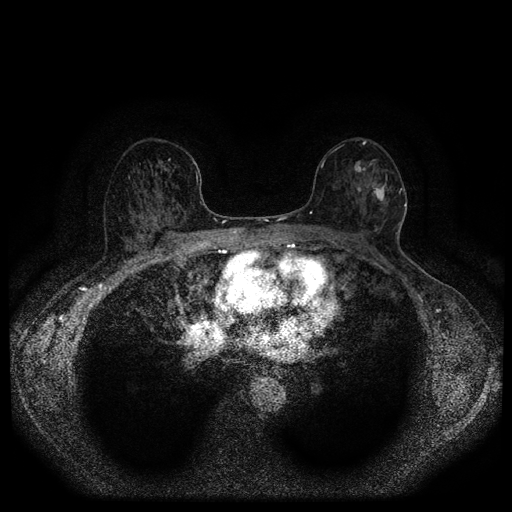
Breast MRI (dynamic contrast-enhanced, multi-phase), one axial slice. Position 60 of 116 along the scan axis. Dynamic contrast-enhanced series, time point 2 of 5 at this slice position (early post-contrast). 1.5 T. TE 2.7 ms, TR 5.4 ms. 2 mm slice thickness. 512 × 512 image matrix. Patient: female, 56 years.
Structures marked on this image (semi-automatically segmented with operator editing):
- breast lesion (labelled 'tumour' in the annotation; benign lesions carry a separate 'benign' label): bounding box [x1, y1, x2, y2] px = [371, 170, 390, 206]